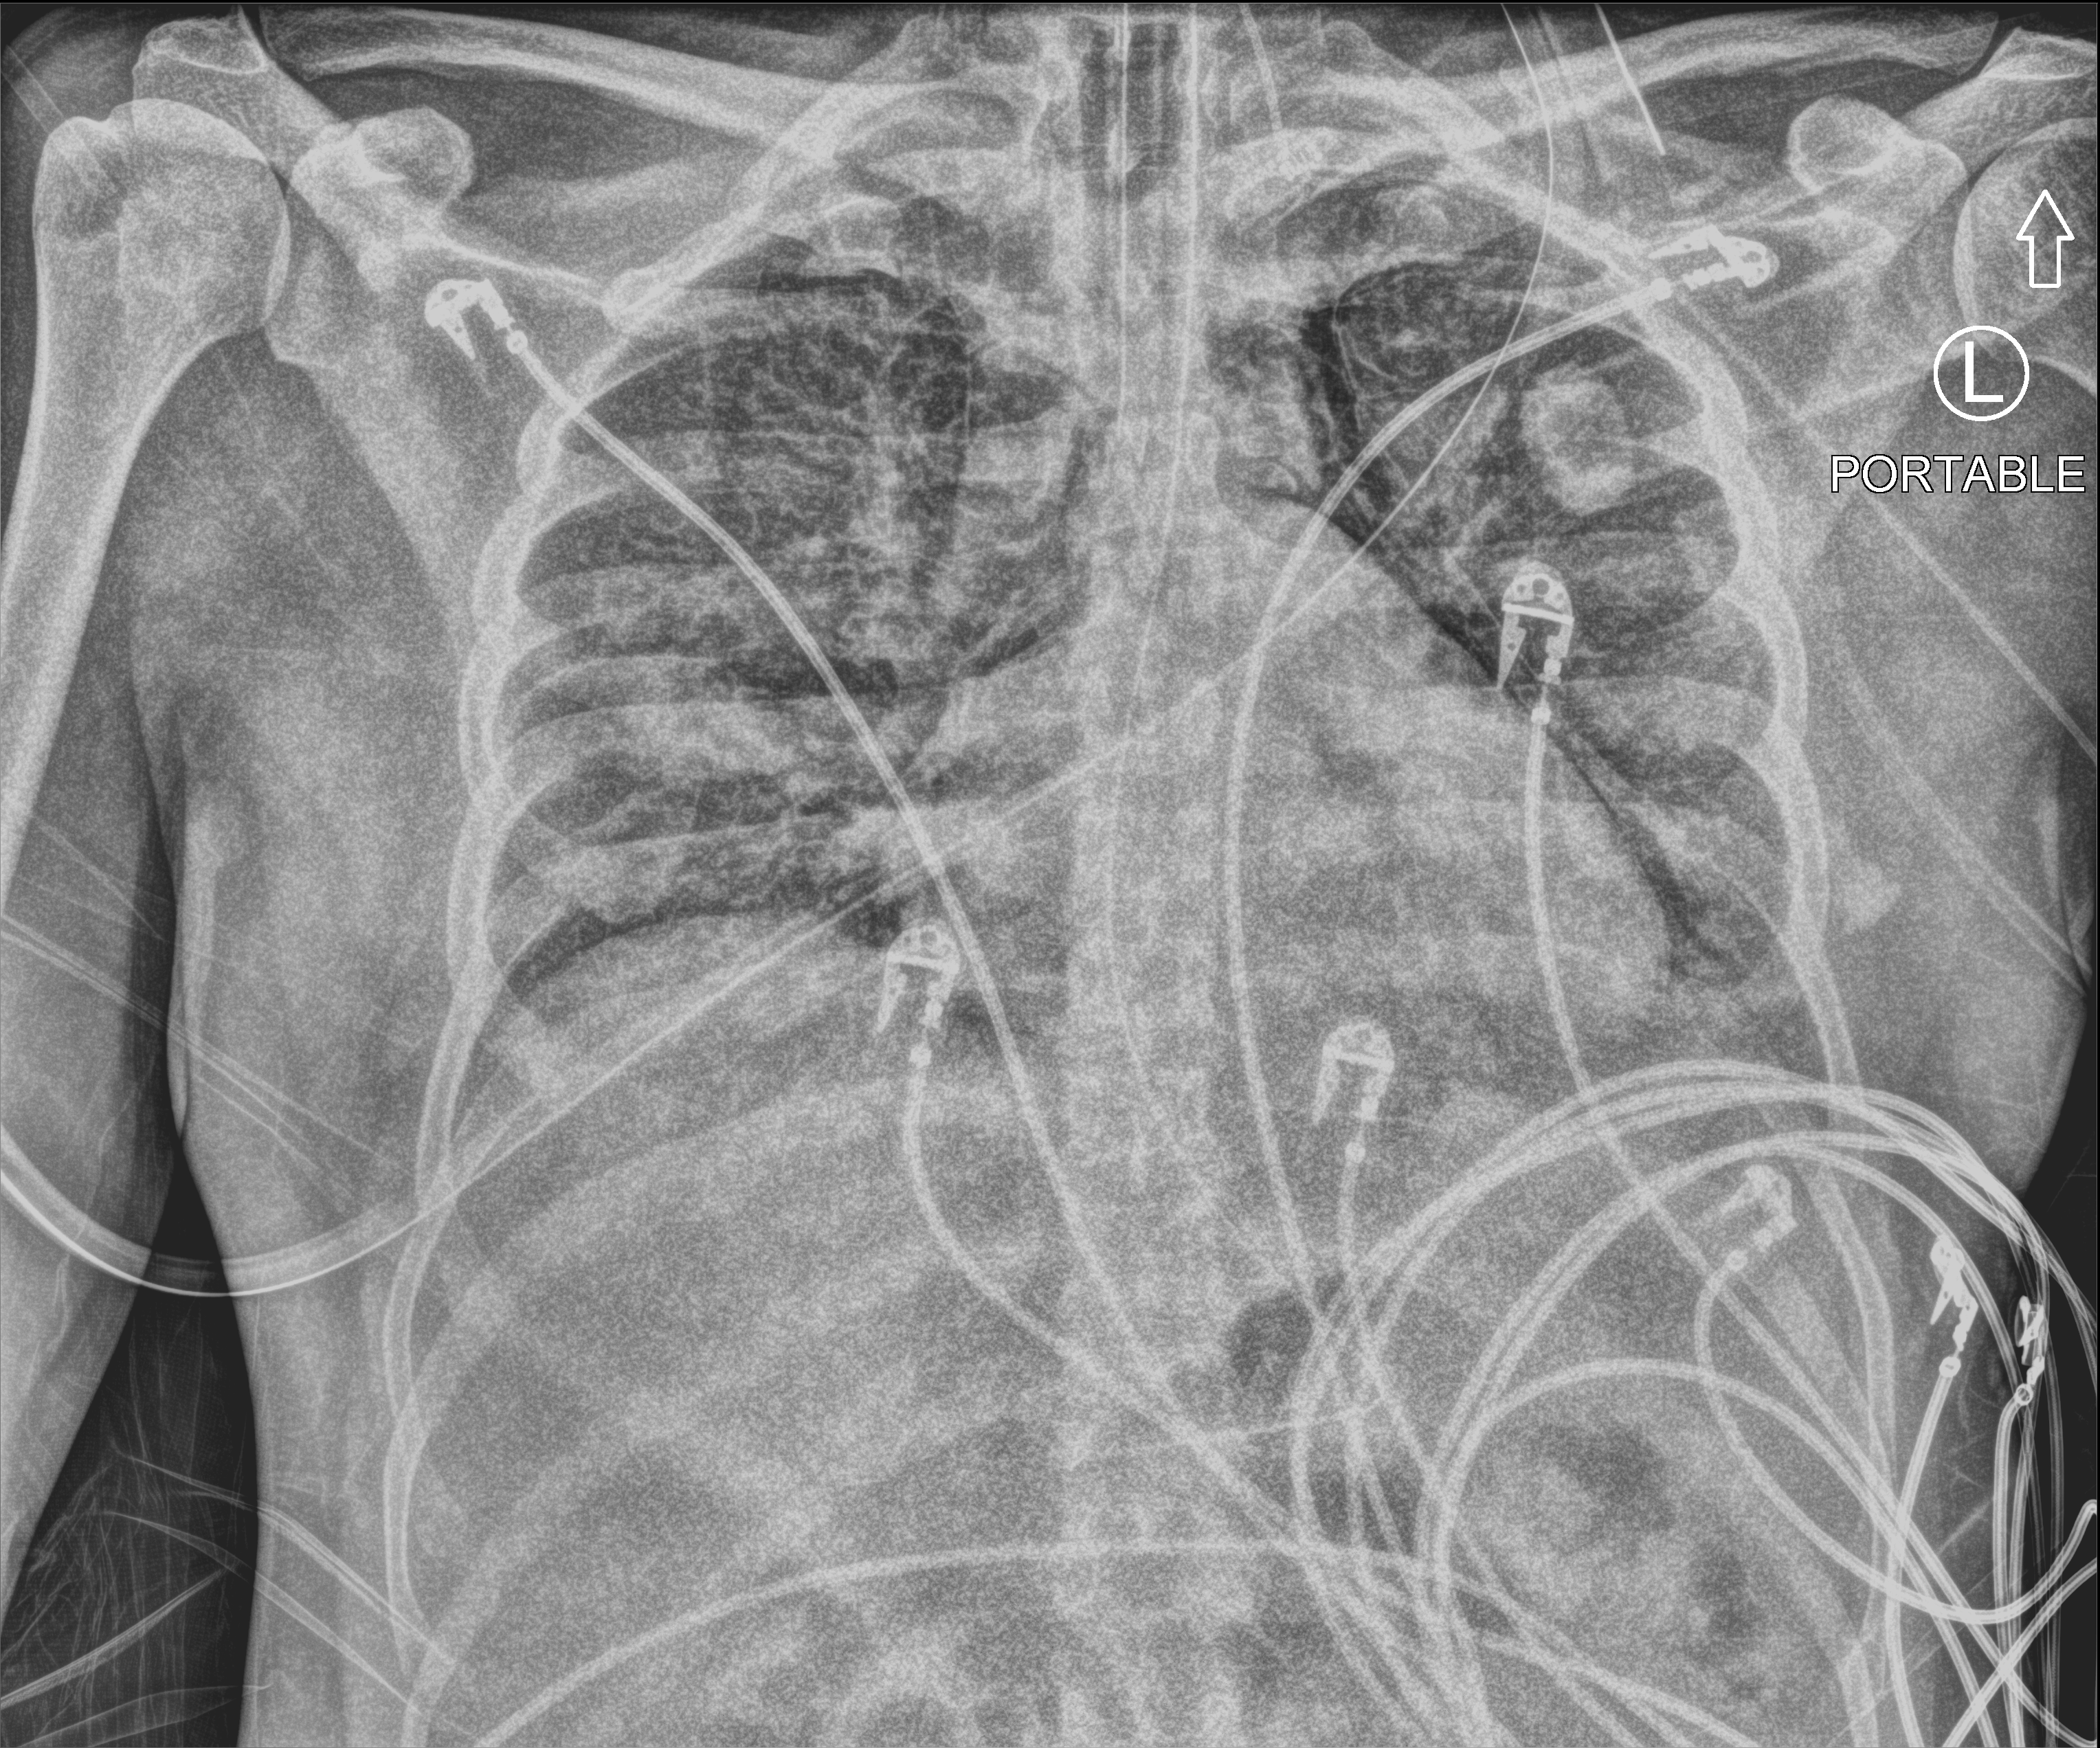
Bedside chest radiograph (computed radiography); anteroposterior (AP) projection. Male patient hospitalised with COVID-19, age 18–59 years.
Hospital-stay facts (about this admission, not read from this image; timing relative to this image not recorded):
- length of hospital stay: 30 days
- mechanically ventilated during this hospital stay: yes
- admitted to intensive care during this hospital stay: yes